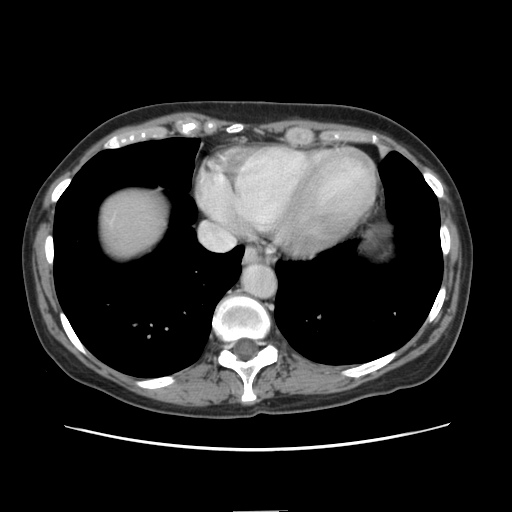
Contrast-enhanced abdominal CT, one axial slice; position 132 of 141 along the scan axis; soft-tissue window (W 400 / L 40 HU); 2.5 mm slice thickness; 512 × 512 image matrix. Female patient, age 63 years. Case-level facts recorded for this patient, not image findings: diagnosis: colorectal cancer liver metastases, imaged before liver resection; multiple liver metastases: yes; largest metastasis: 3.2 cm; disease in both lobes: yes.
Annotated regions visible in this slice (manually delineated by an expert):
- liver: box from (x=99, y=189) to (x=167, y=262) px